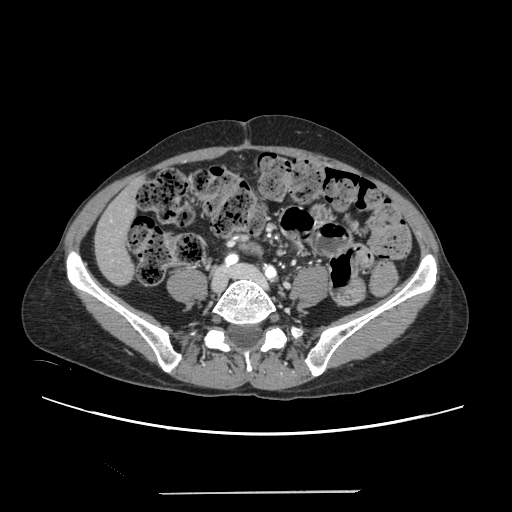
Contrast-enhanced abdominal CT, one axial slice. Slice 25 of 240 in the series (ordered by position). 120 kVp. Soft-tissue window (W 400 / L 40 HU). 1.25 mm slice thickness. 512 × 512 image matrix. Female patient, age 60 years. Case-level facts recorded for this patient, not image findings: diagnosis: colorectal cancer liver metastases, imaged before liver resection; multiple liver metastases: no; largest metastasis: 1.5 cm; disease in both lobes: no.
Structures marked on this image (outlined manually by an expert reader):
- liver: box from (x=96, y=183) to (x=137, y=283) px
- planned liver remnant (the part of the liver to remain after resection): (x=96, y=183)–(x=137, y=284)
- portal vein (with intrahepatic branches): (x=109, y=219)–(x=112, y=222)